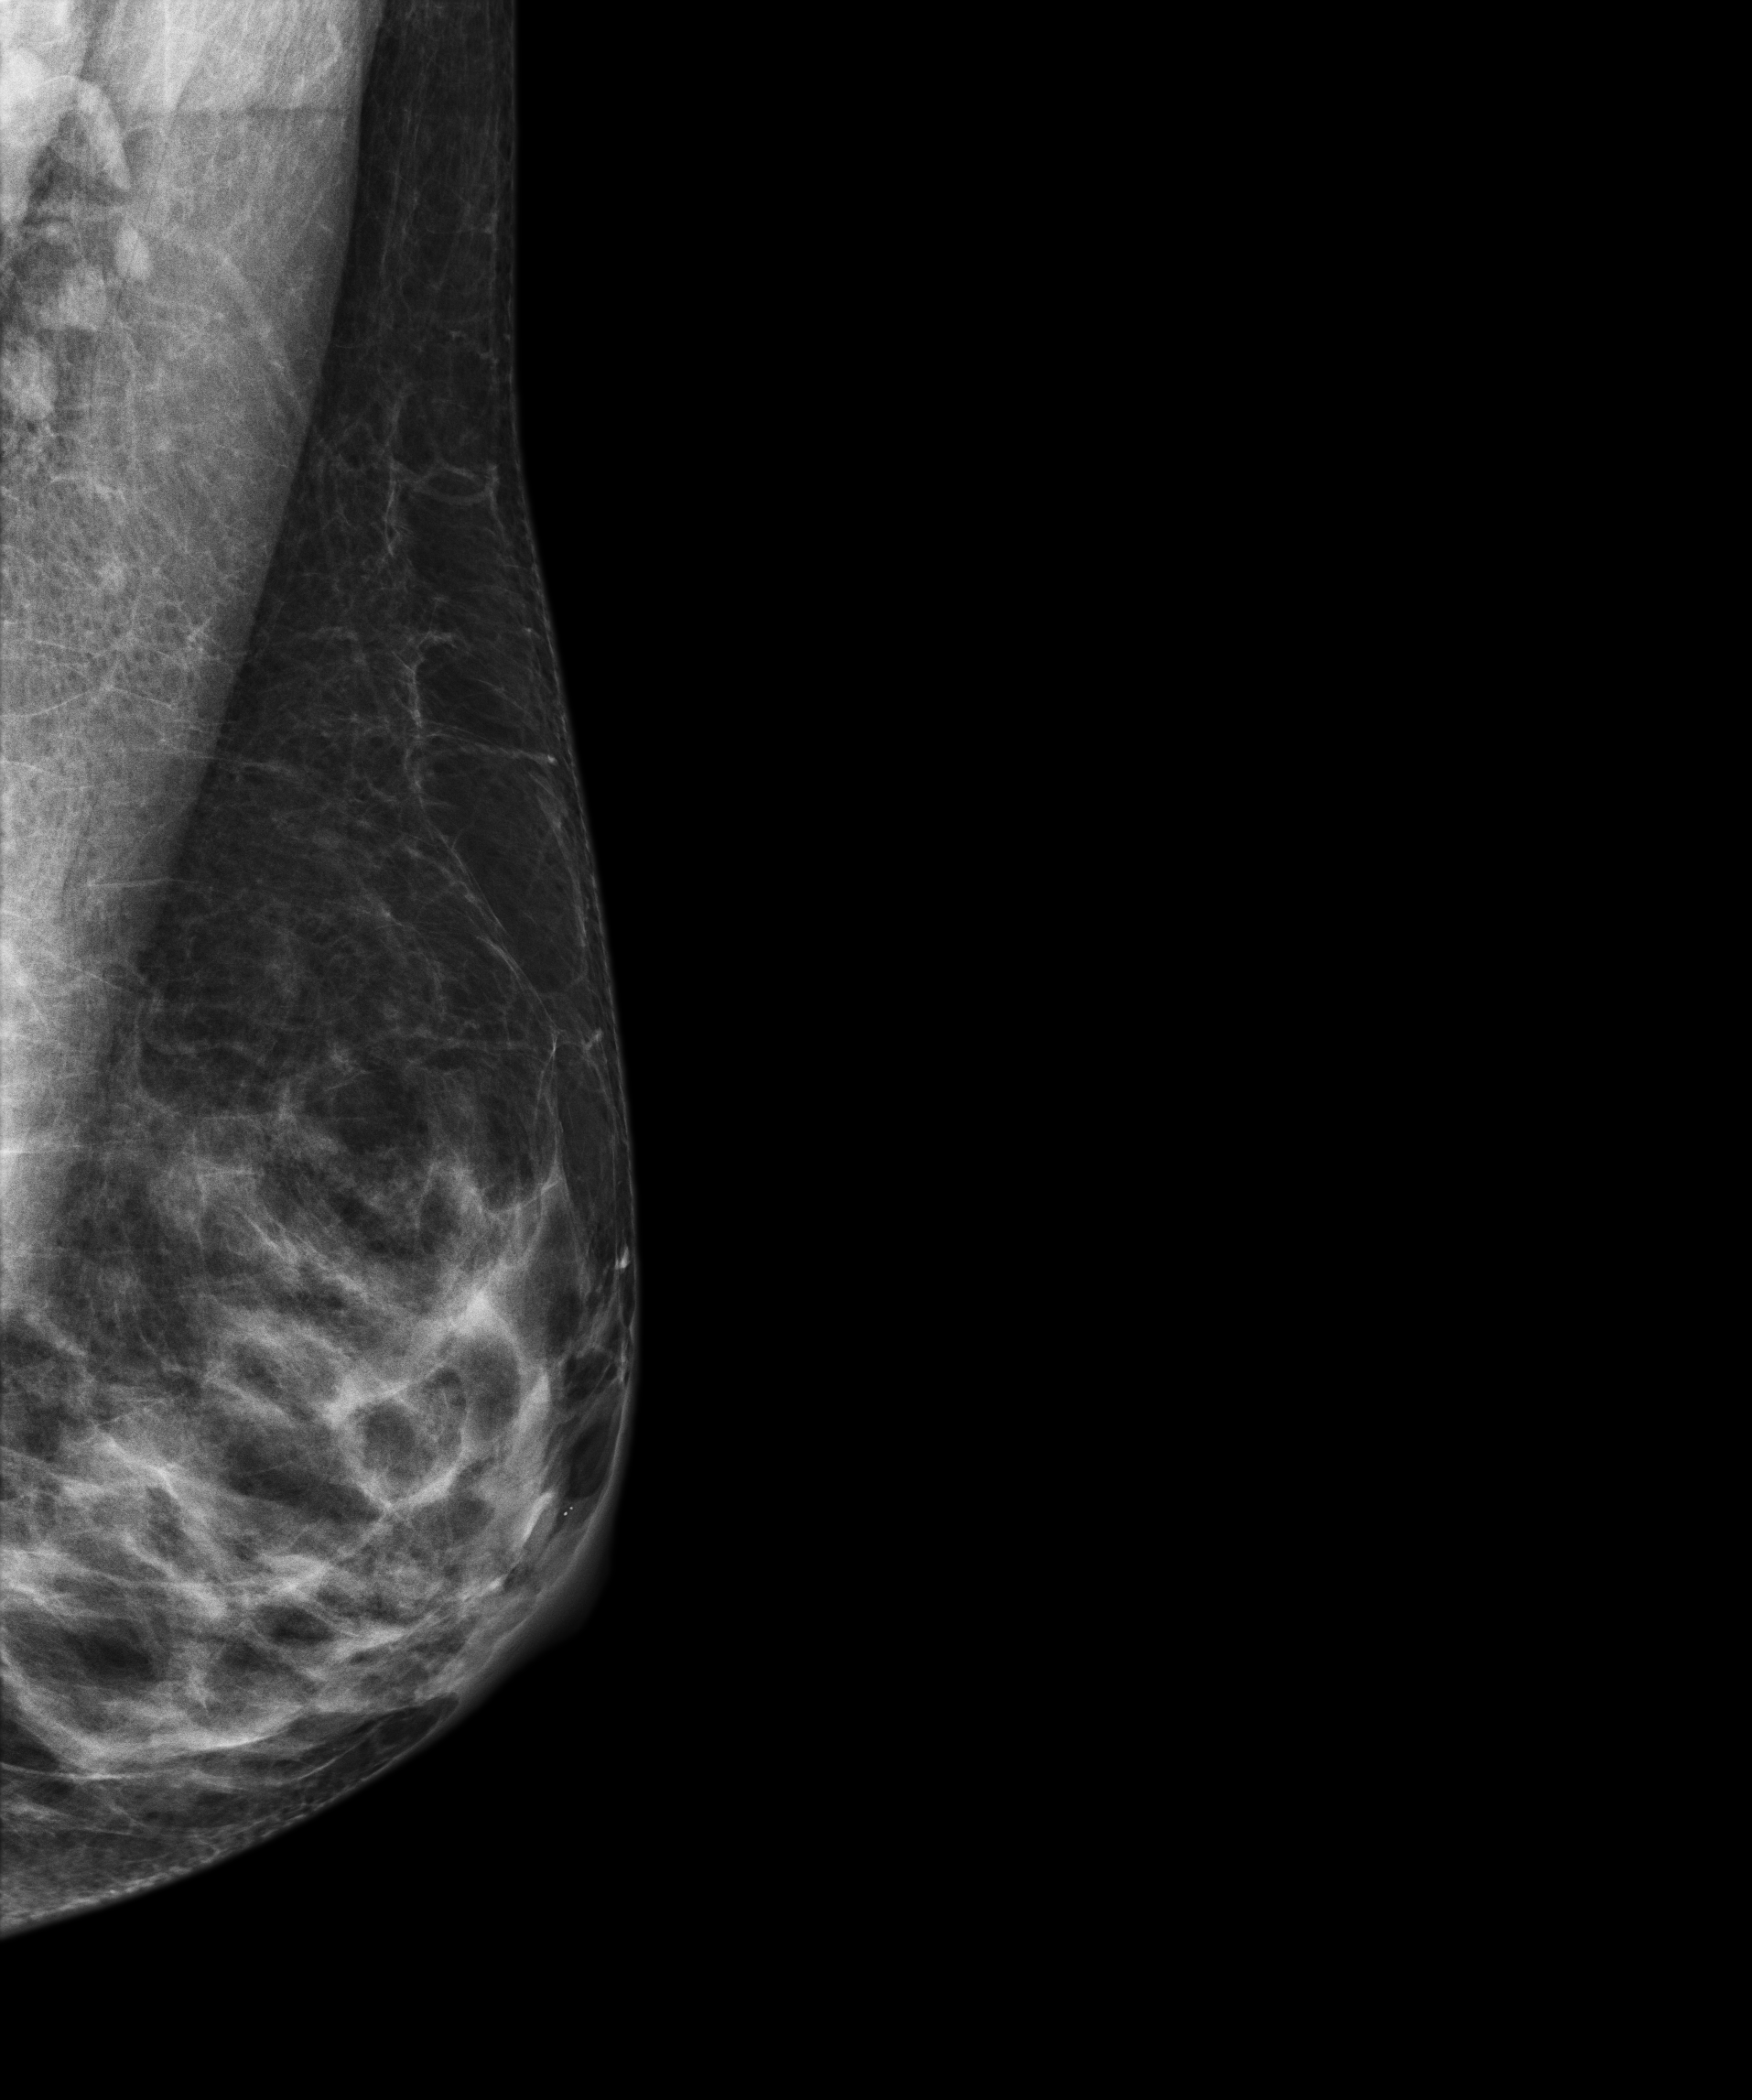
Full-field digital mammogram (FFDM); left breast; mediolateral oblique (MLO) view; screening examination; compressed breast thickness 50 mm; system: Senographe Essential ADS_56.21.3. Patient aged 66 years (female).
Final BI-RADS assessment for this screening round (tomosynthesis exam, both breasts): category 1.